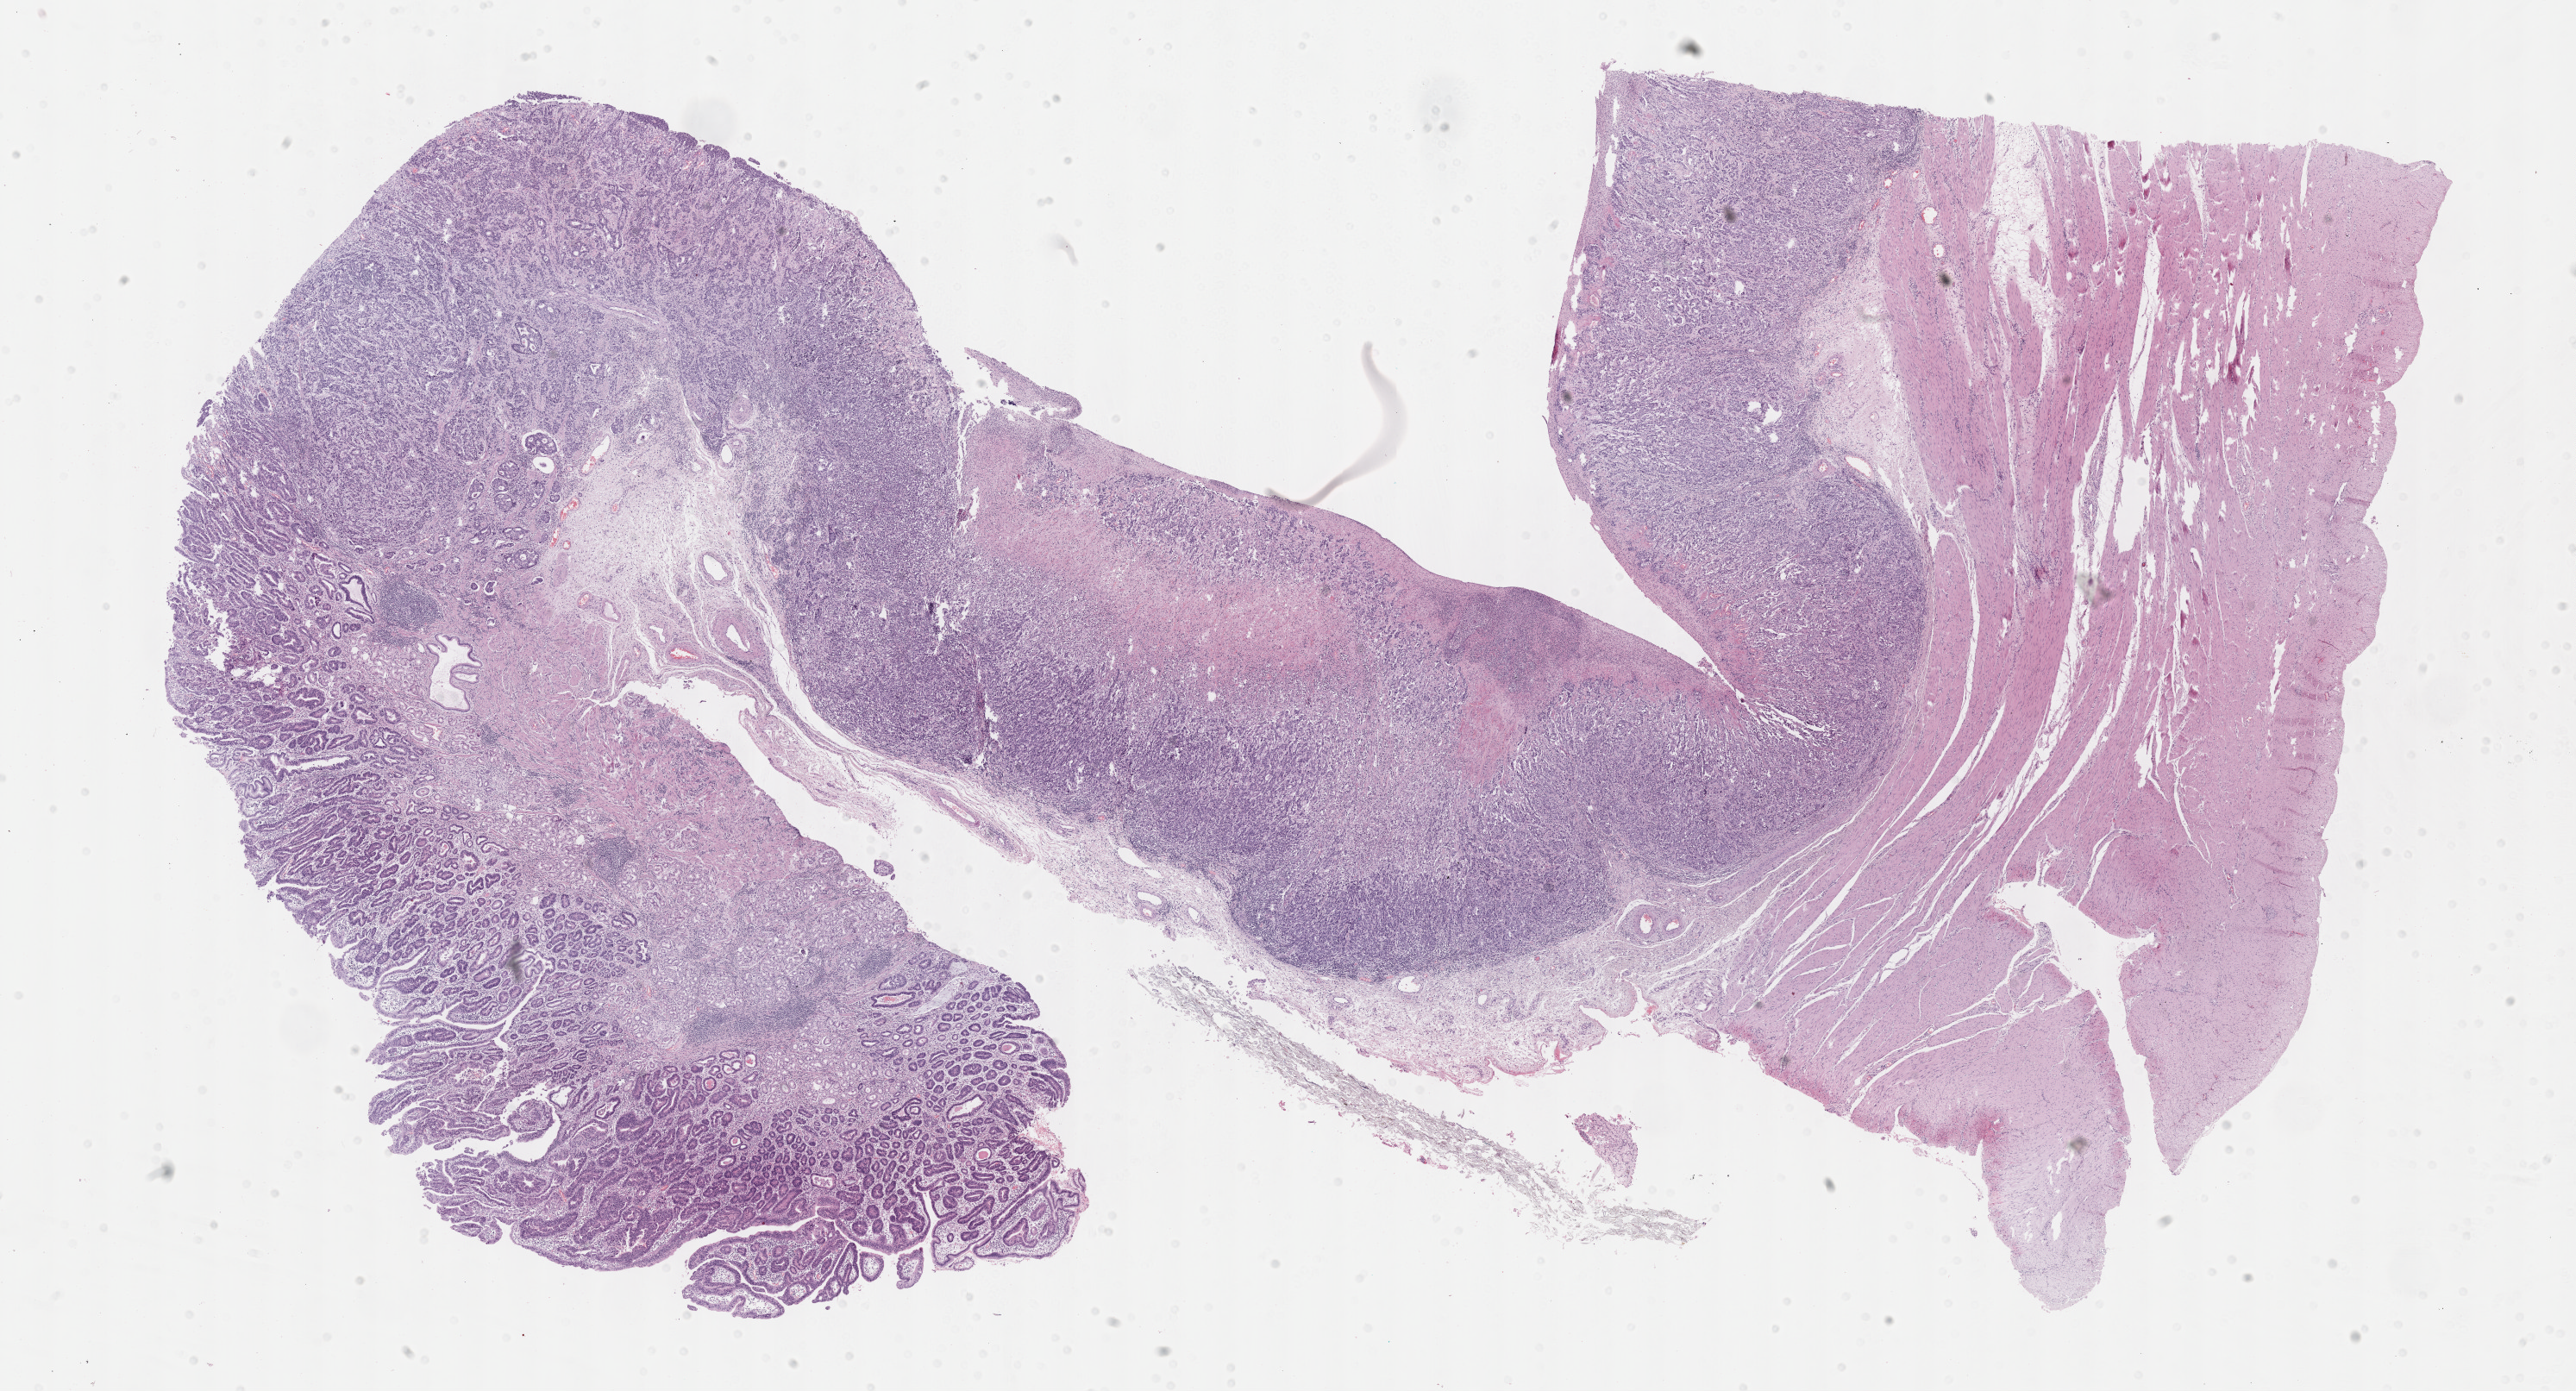
Whole-slide histology image, H&E-stained — a low-resolution overview of the entire scanned area, about 24.2 x 13.0 mm (slide scanned at 40x). FFPE section. Primary tumour sample from the stomach. Female patient; age at initial diagnosis 71 years. Histologic grade: G3 (poorly differentiated).
Lymph nodes positive (case pathology): 3 of 17 examined. AJCC pathologic stage: IIB. Pathologic diagnosis: Adenocarcinoma, NOS (gastric antrum).